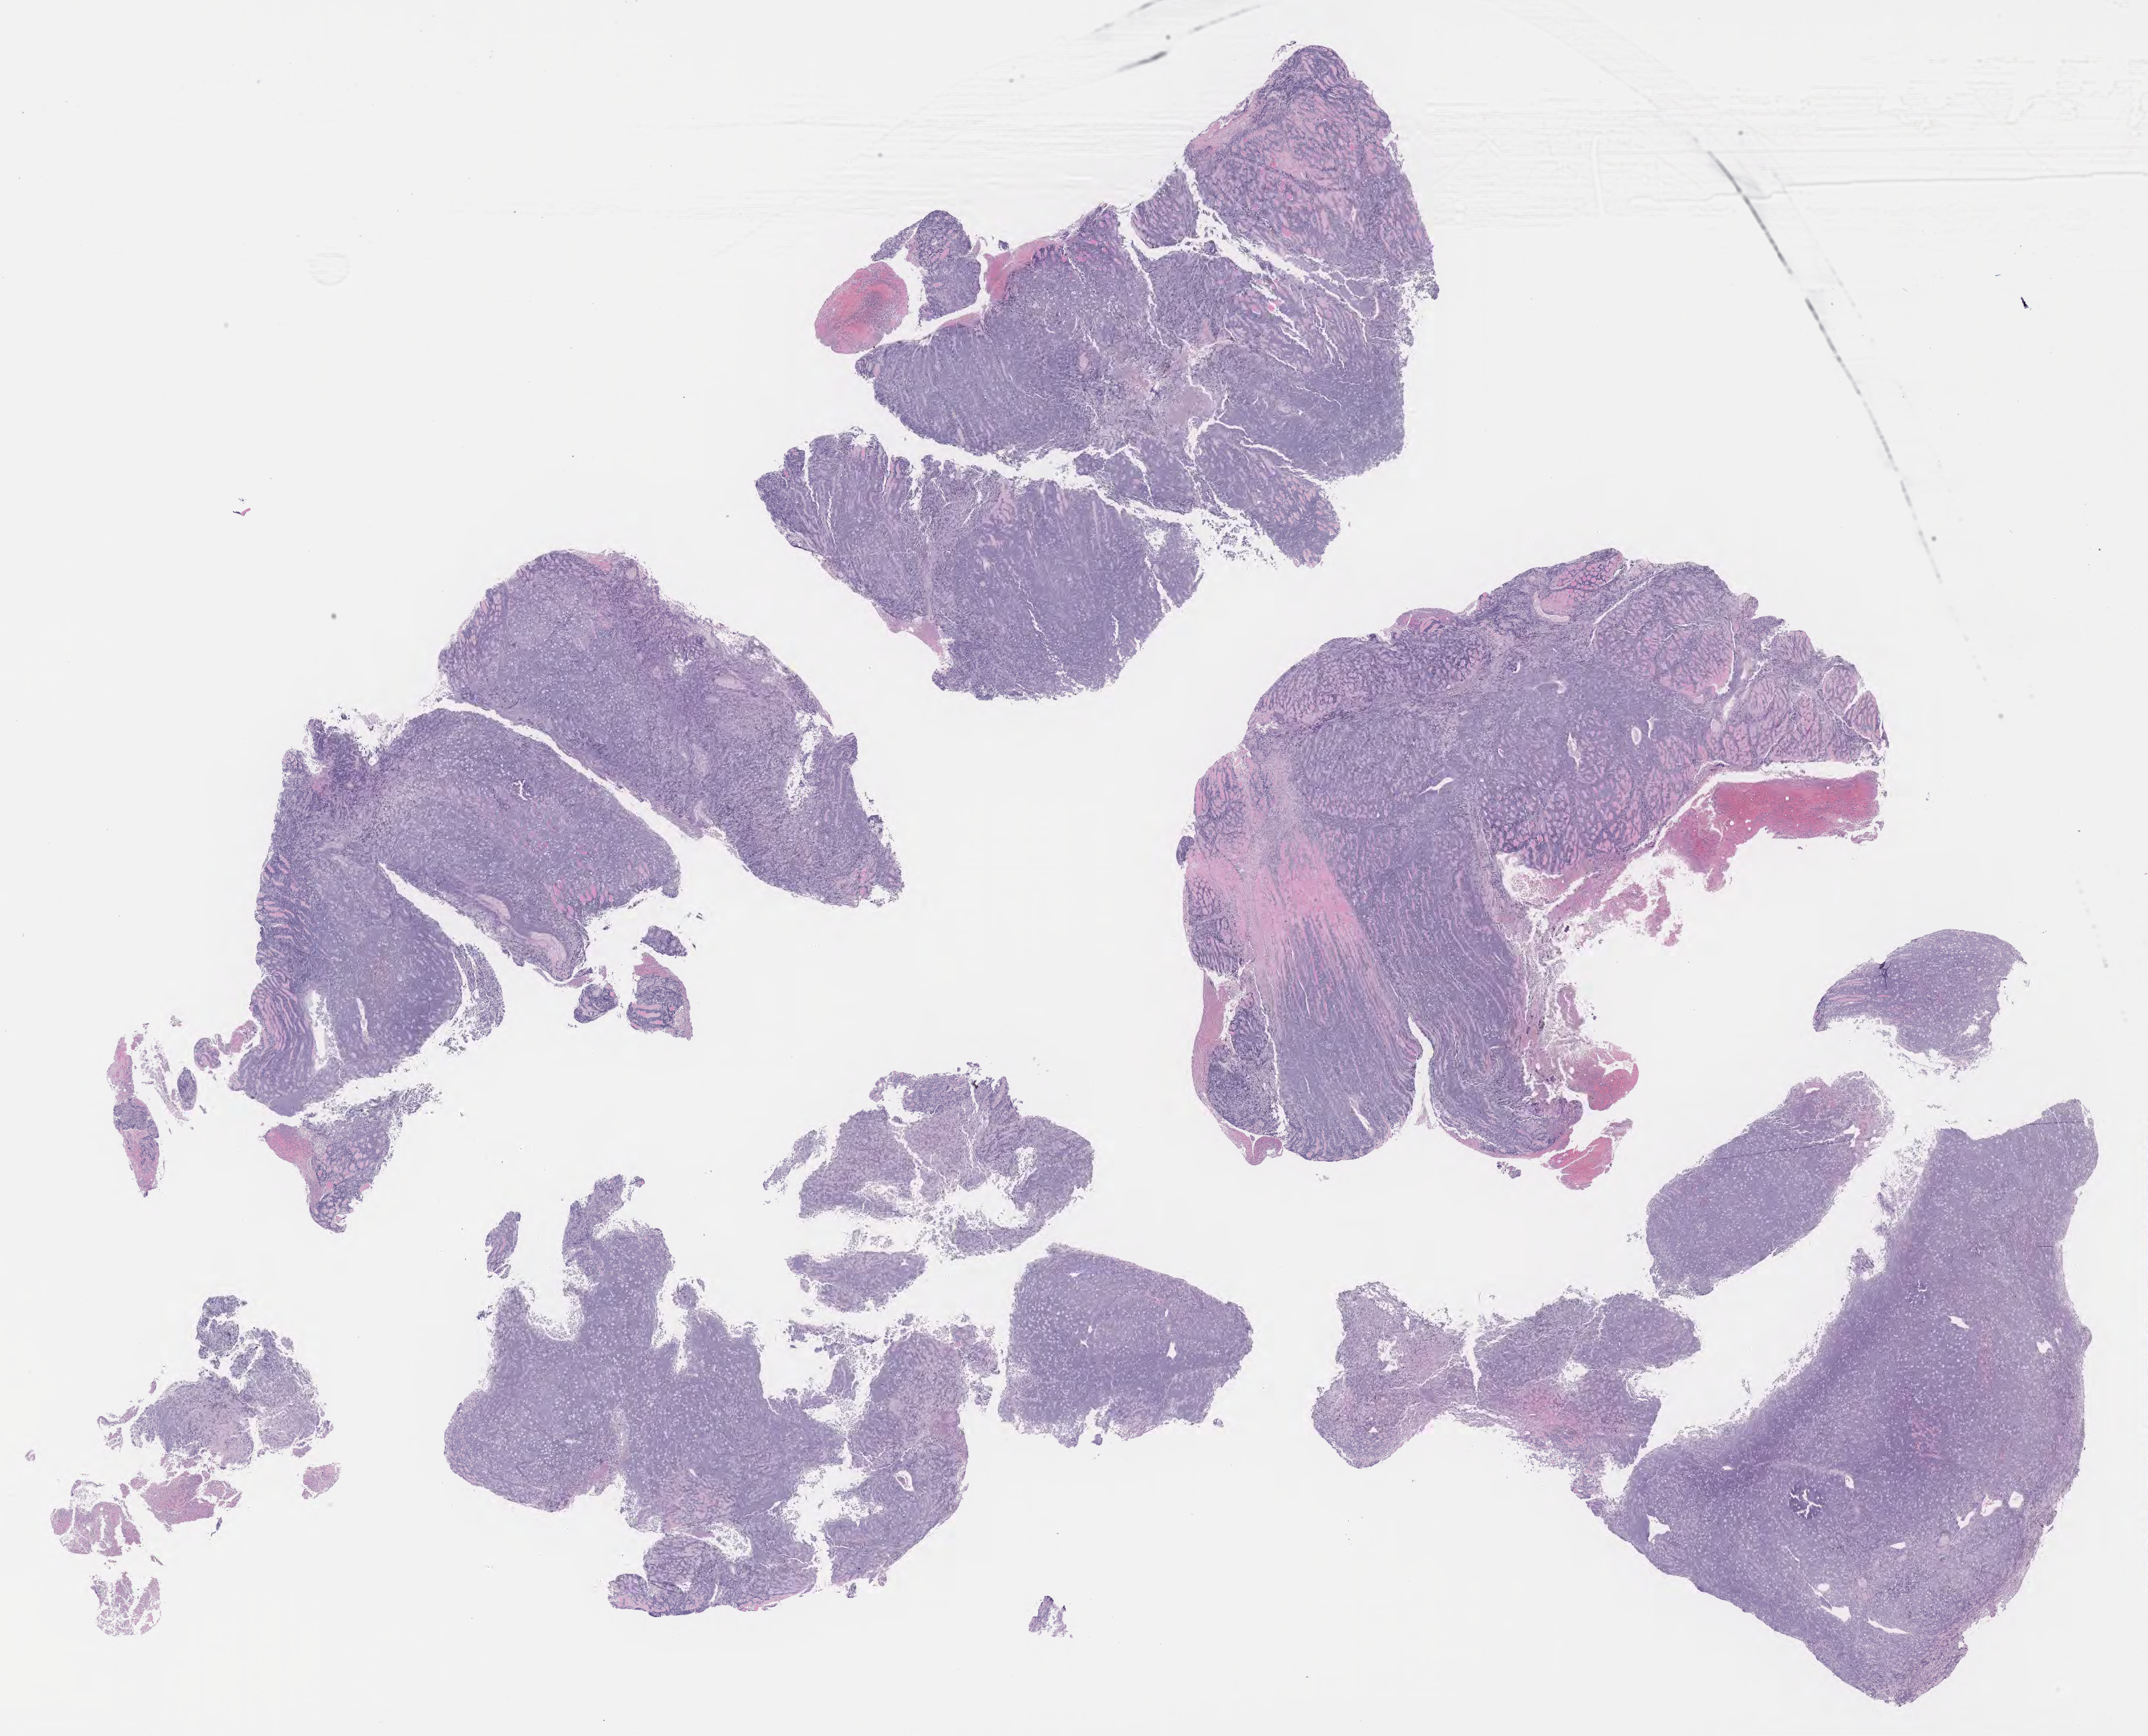
Whole-slide image, haematoxylin and eosin stain, shown as a low-resolution overview of the whole scanned area (about 26.2 x 21.1 mm); tumor tissue. Patient: female, 29 years old.
Diagnosis: Burkitt lymphoma, NOS.